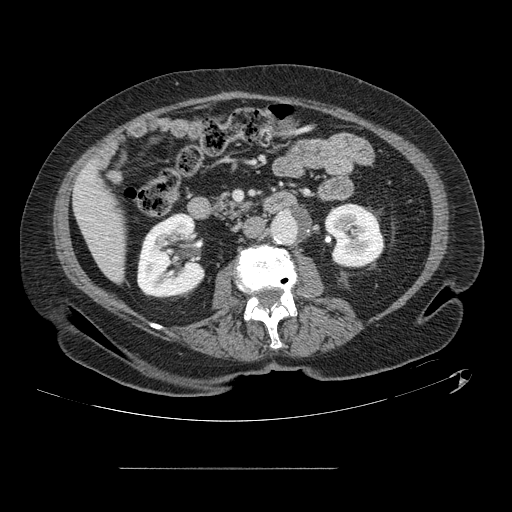
Contrast-enhanced abdominal CT, one axial slice; slice 31 of 148 in the series (ordered by position); 120 kVp; intravenous contrast given; soft-tissue window (W 400 / L 40 HU); 512 × 512 image matrix, field of view 439 × 439 mm. Female patient, age 75 years. Case-level facts recorded for this patient, not image findings: diagnosis: colorectal cancer liver metastases, imaged before liver resection; multiple liver metastases: no; largest metastasis: 2.4 cm; disease in both lobes: no.
Annotated regions visible in this slice (expert manual segmentation):
- liver: bounding box (x1, y1, x2, y2) in pixels: (75, 165, 125, 281)
- planned liver remnant (the part of the liver to remain after resection): (75, 166, 125, 281)